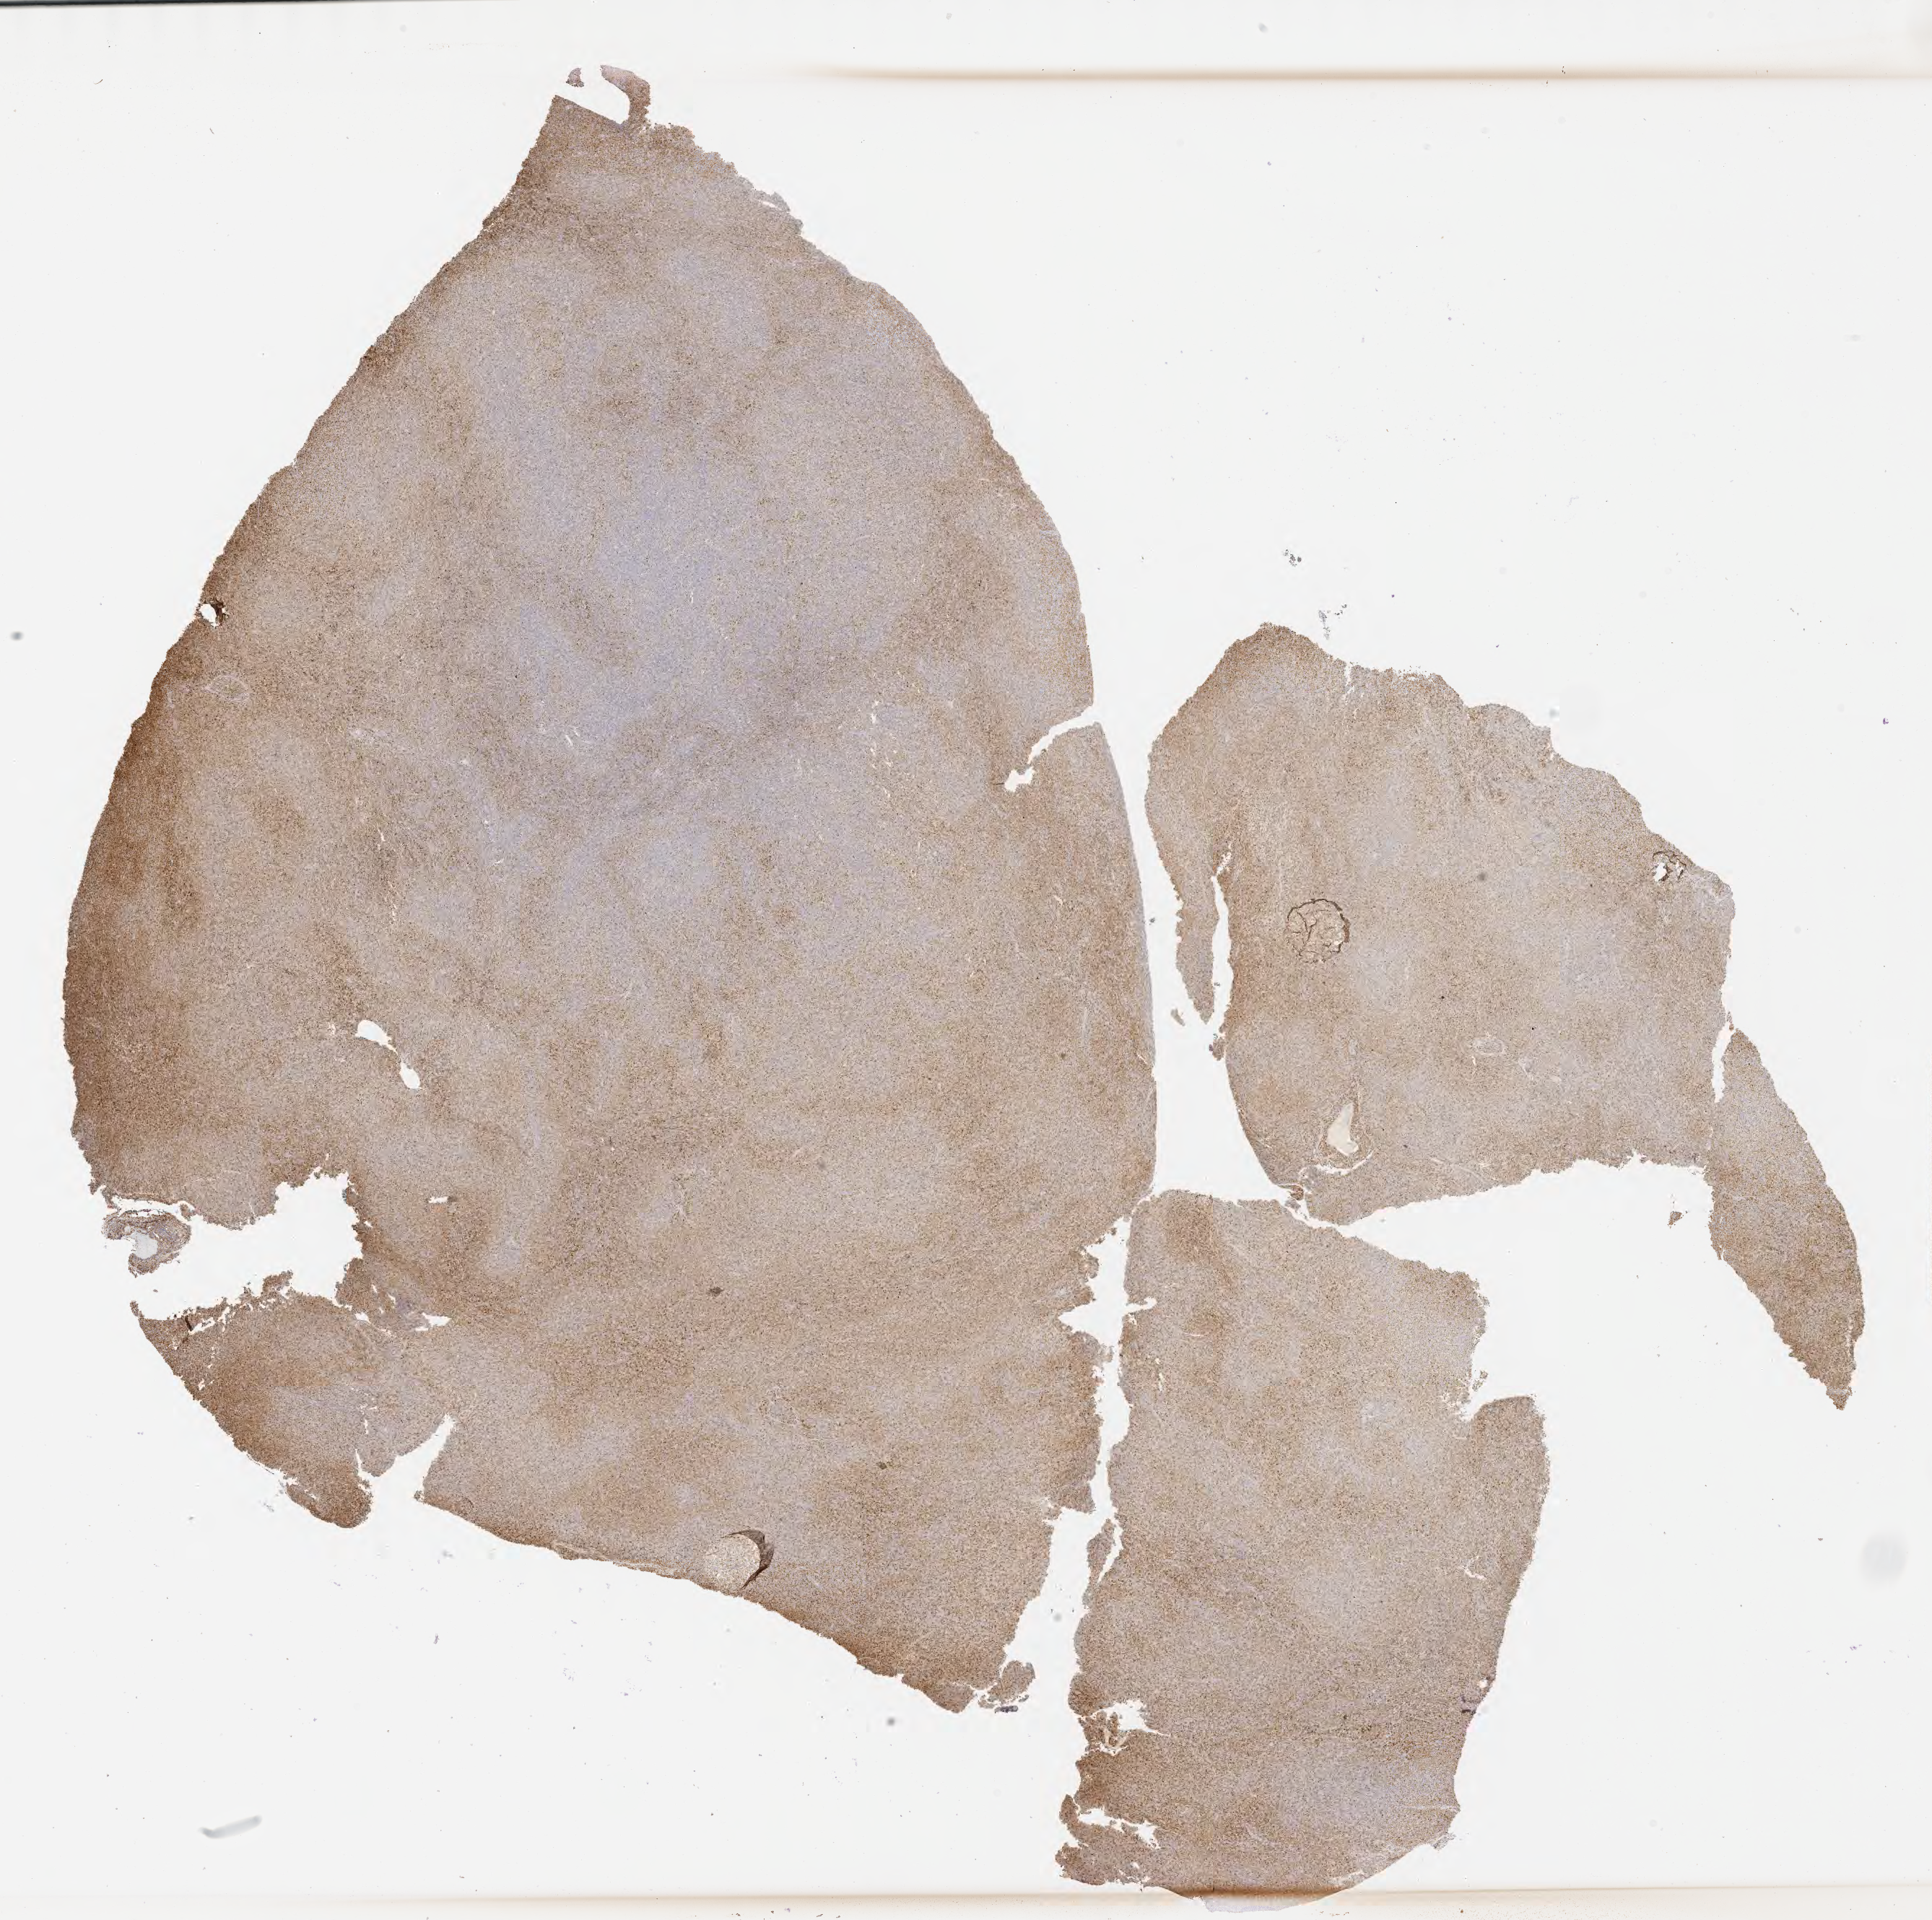
Immunohistochemistry (IHC) whole-slide image stained for CD79a, whole scanned area (about 21.6 x 21.5 mm) shown as a low-resolution overview, tumor tissue, site: liver. Patient: female, aged 46.
Histologic diagnosis: Diffuse large B-cell lymphoma, NOS.